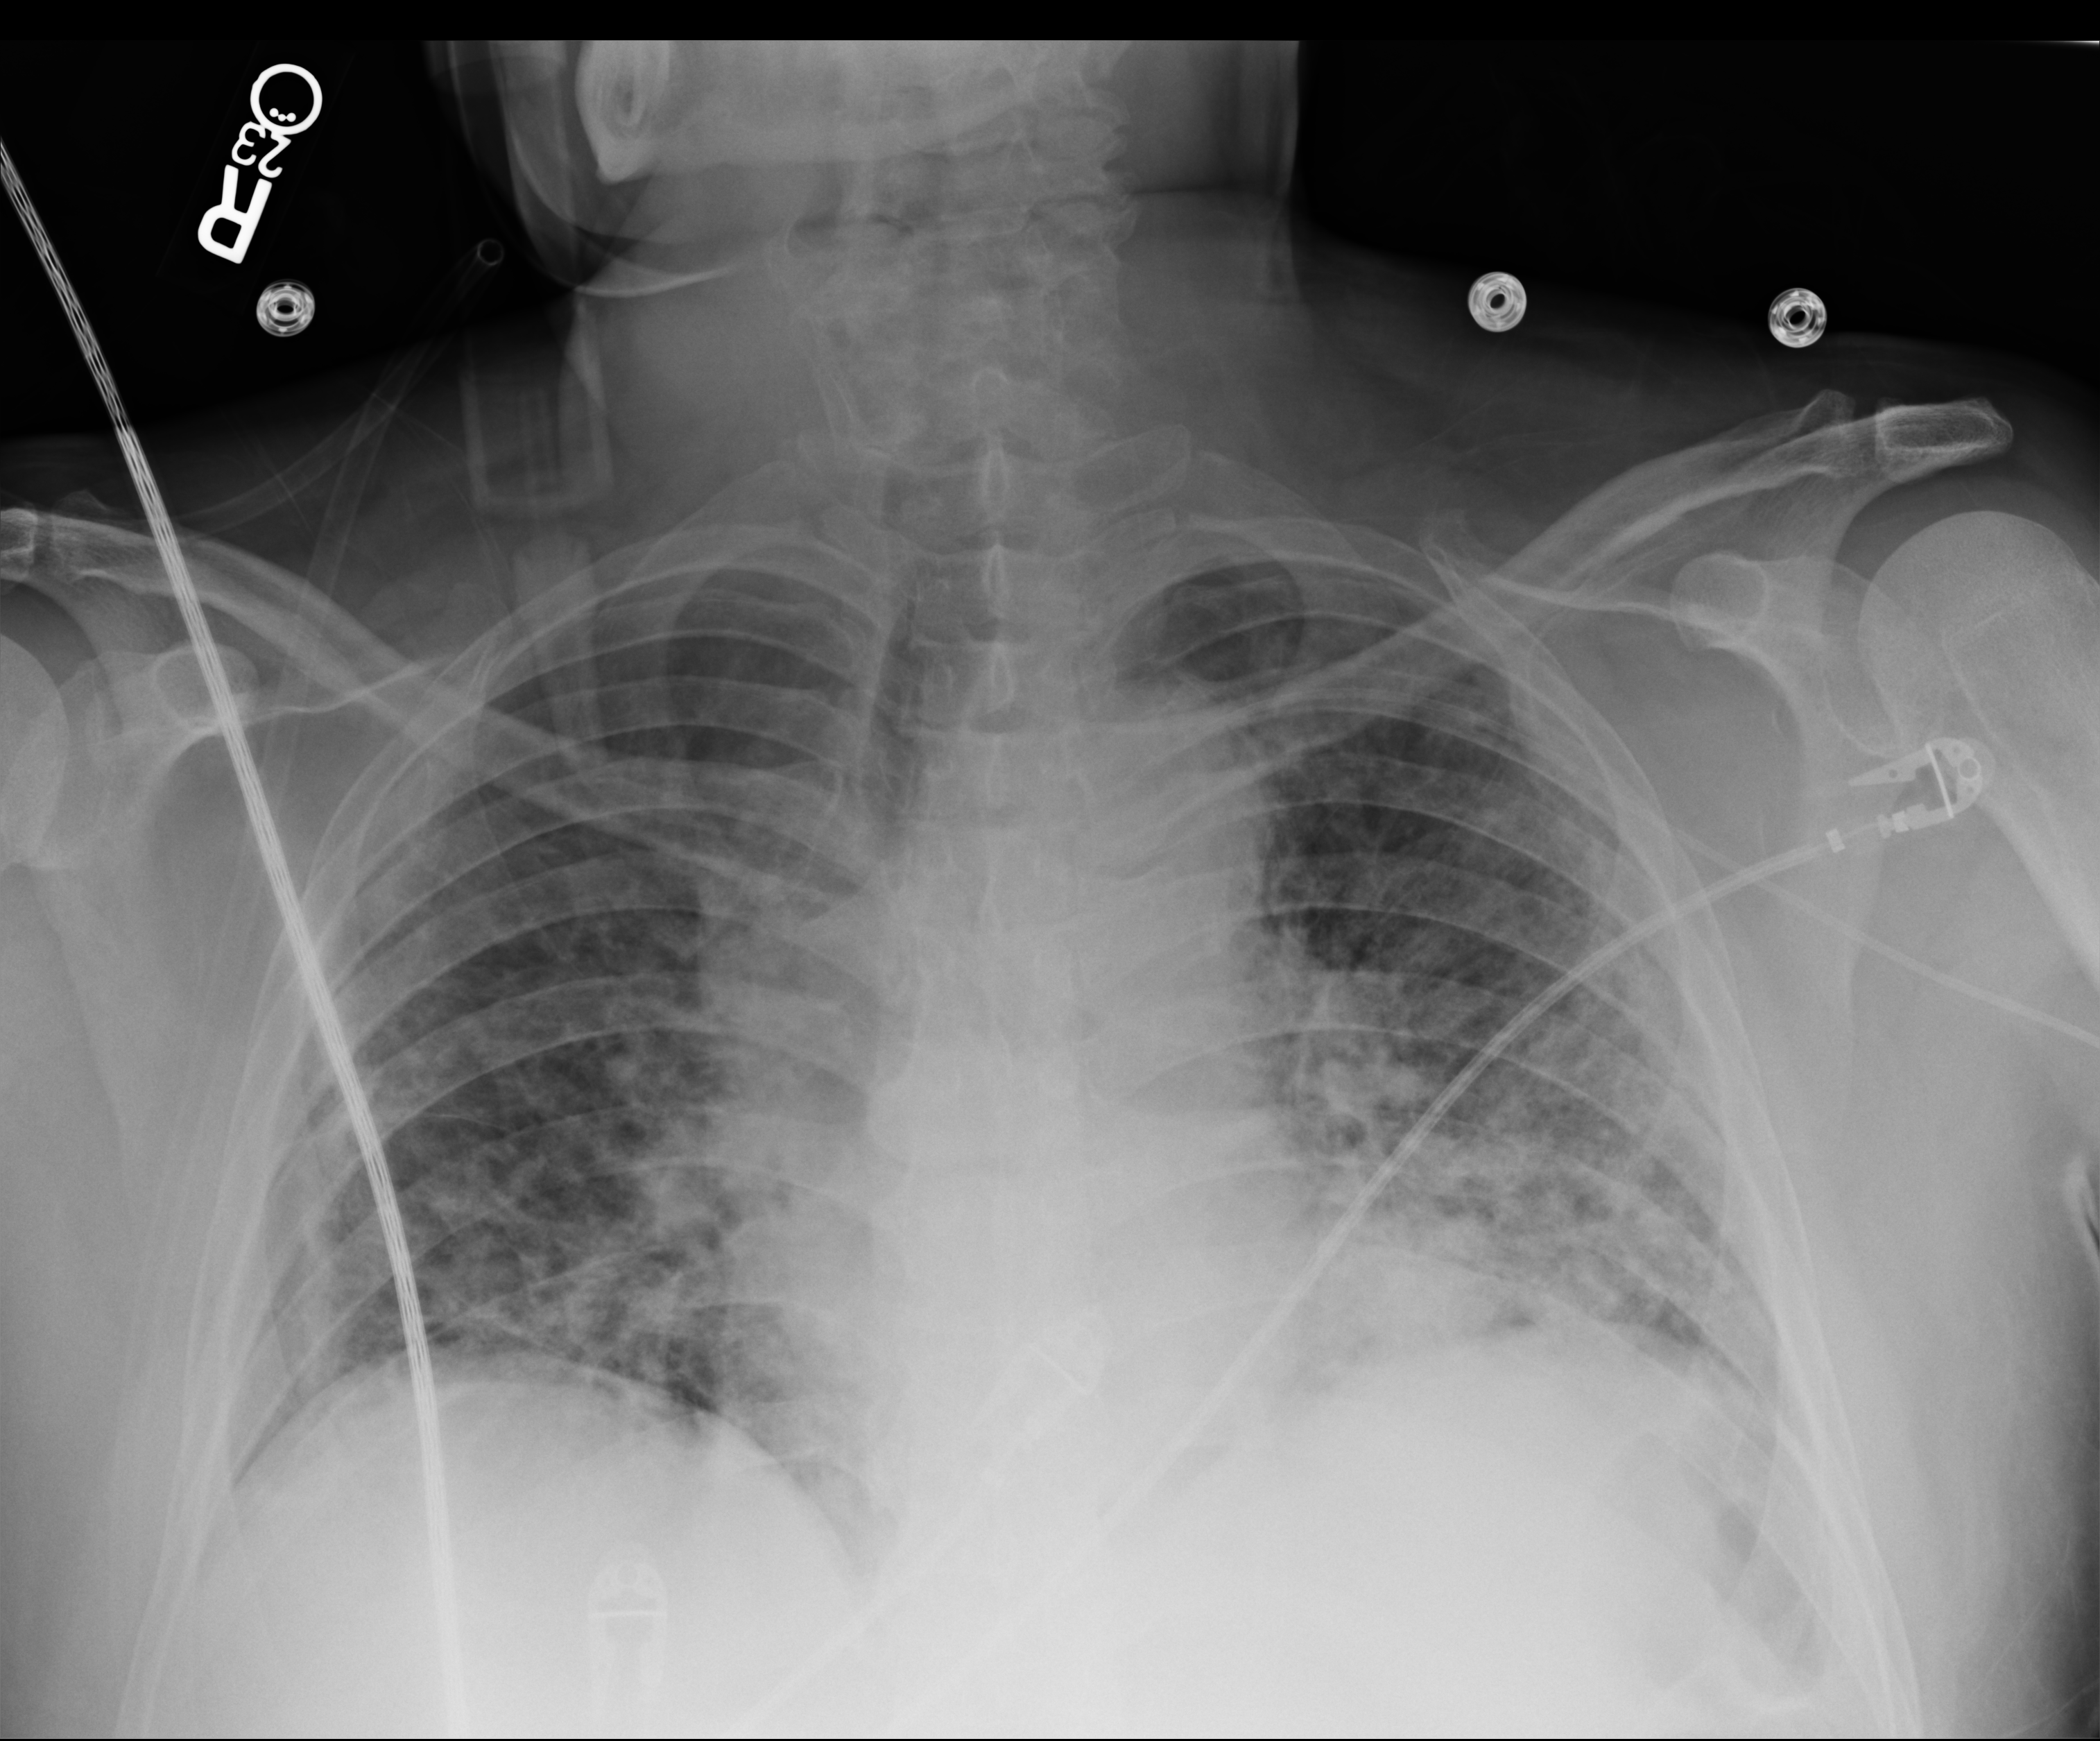
Bedside chest radiograph (computed radiography); anteroposterior (AP) projection. Patient hospitalised with COVID-19; male, aged 60–74 years.
Hospital-stay facts (about this admission, not read from this image; timing relative to this image not recorded): mechanically ventilated during this hospital stay: yes; admitted to intensive care during this hospital stay: yes.